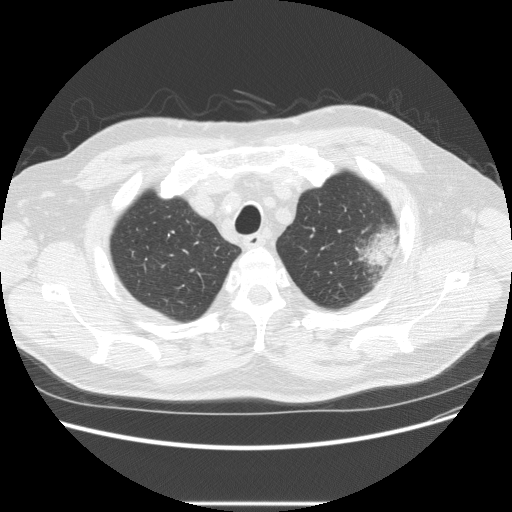
Low-dose screening chest CT, axial slice; baseline screening round; lung window (W 1500 / L -600 HU); 2.5 mm slice thickness; slice 41 of 233 in the series. Male participant, aged 73 years at enrolment. Former smoker at enrolment.
- Lesion marked by an expert reader, bounding box (x1, y1, x2, y2) in pixels: (332, 216, 407, 283).
- The screening reader recorded 2 non-calcified nodules or masses ≥4 mm on this exam (left upper lobe, right upper lobe); which of them this box marks is not recorded.
- Lung cancer was diagnosed 11 days after this screen: bronchiolo-alveolar adenocarcinoma, NOS, other location, well differentiated (G1), stage IV (AJCC 6th edition).